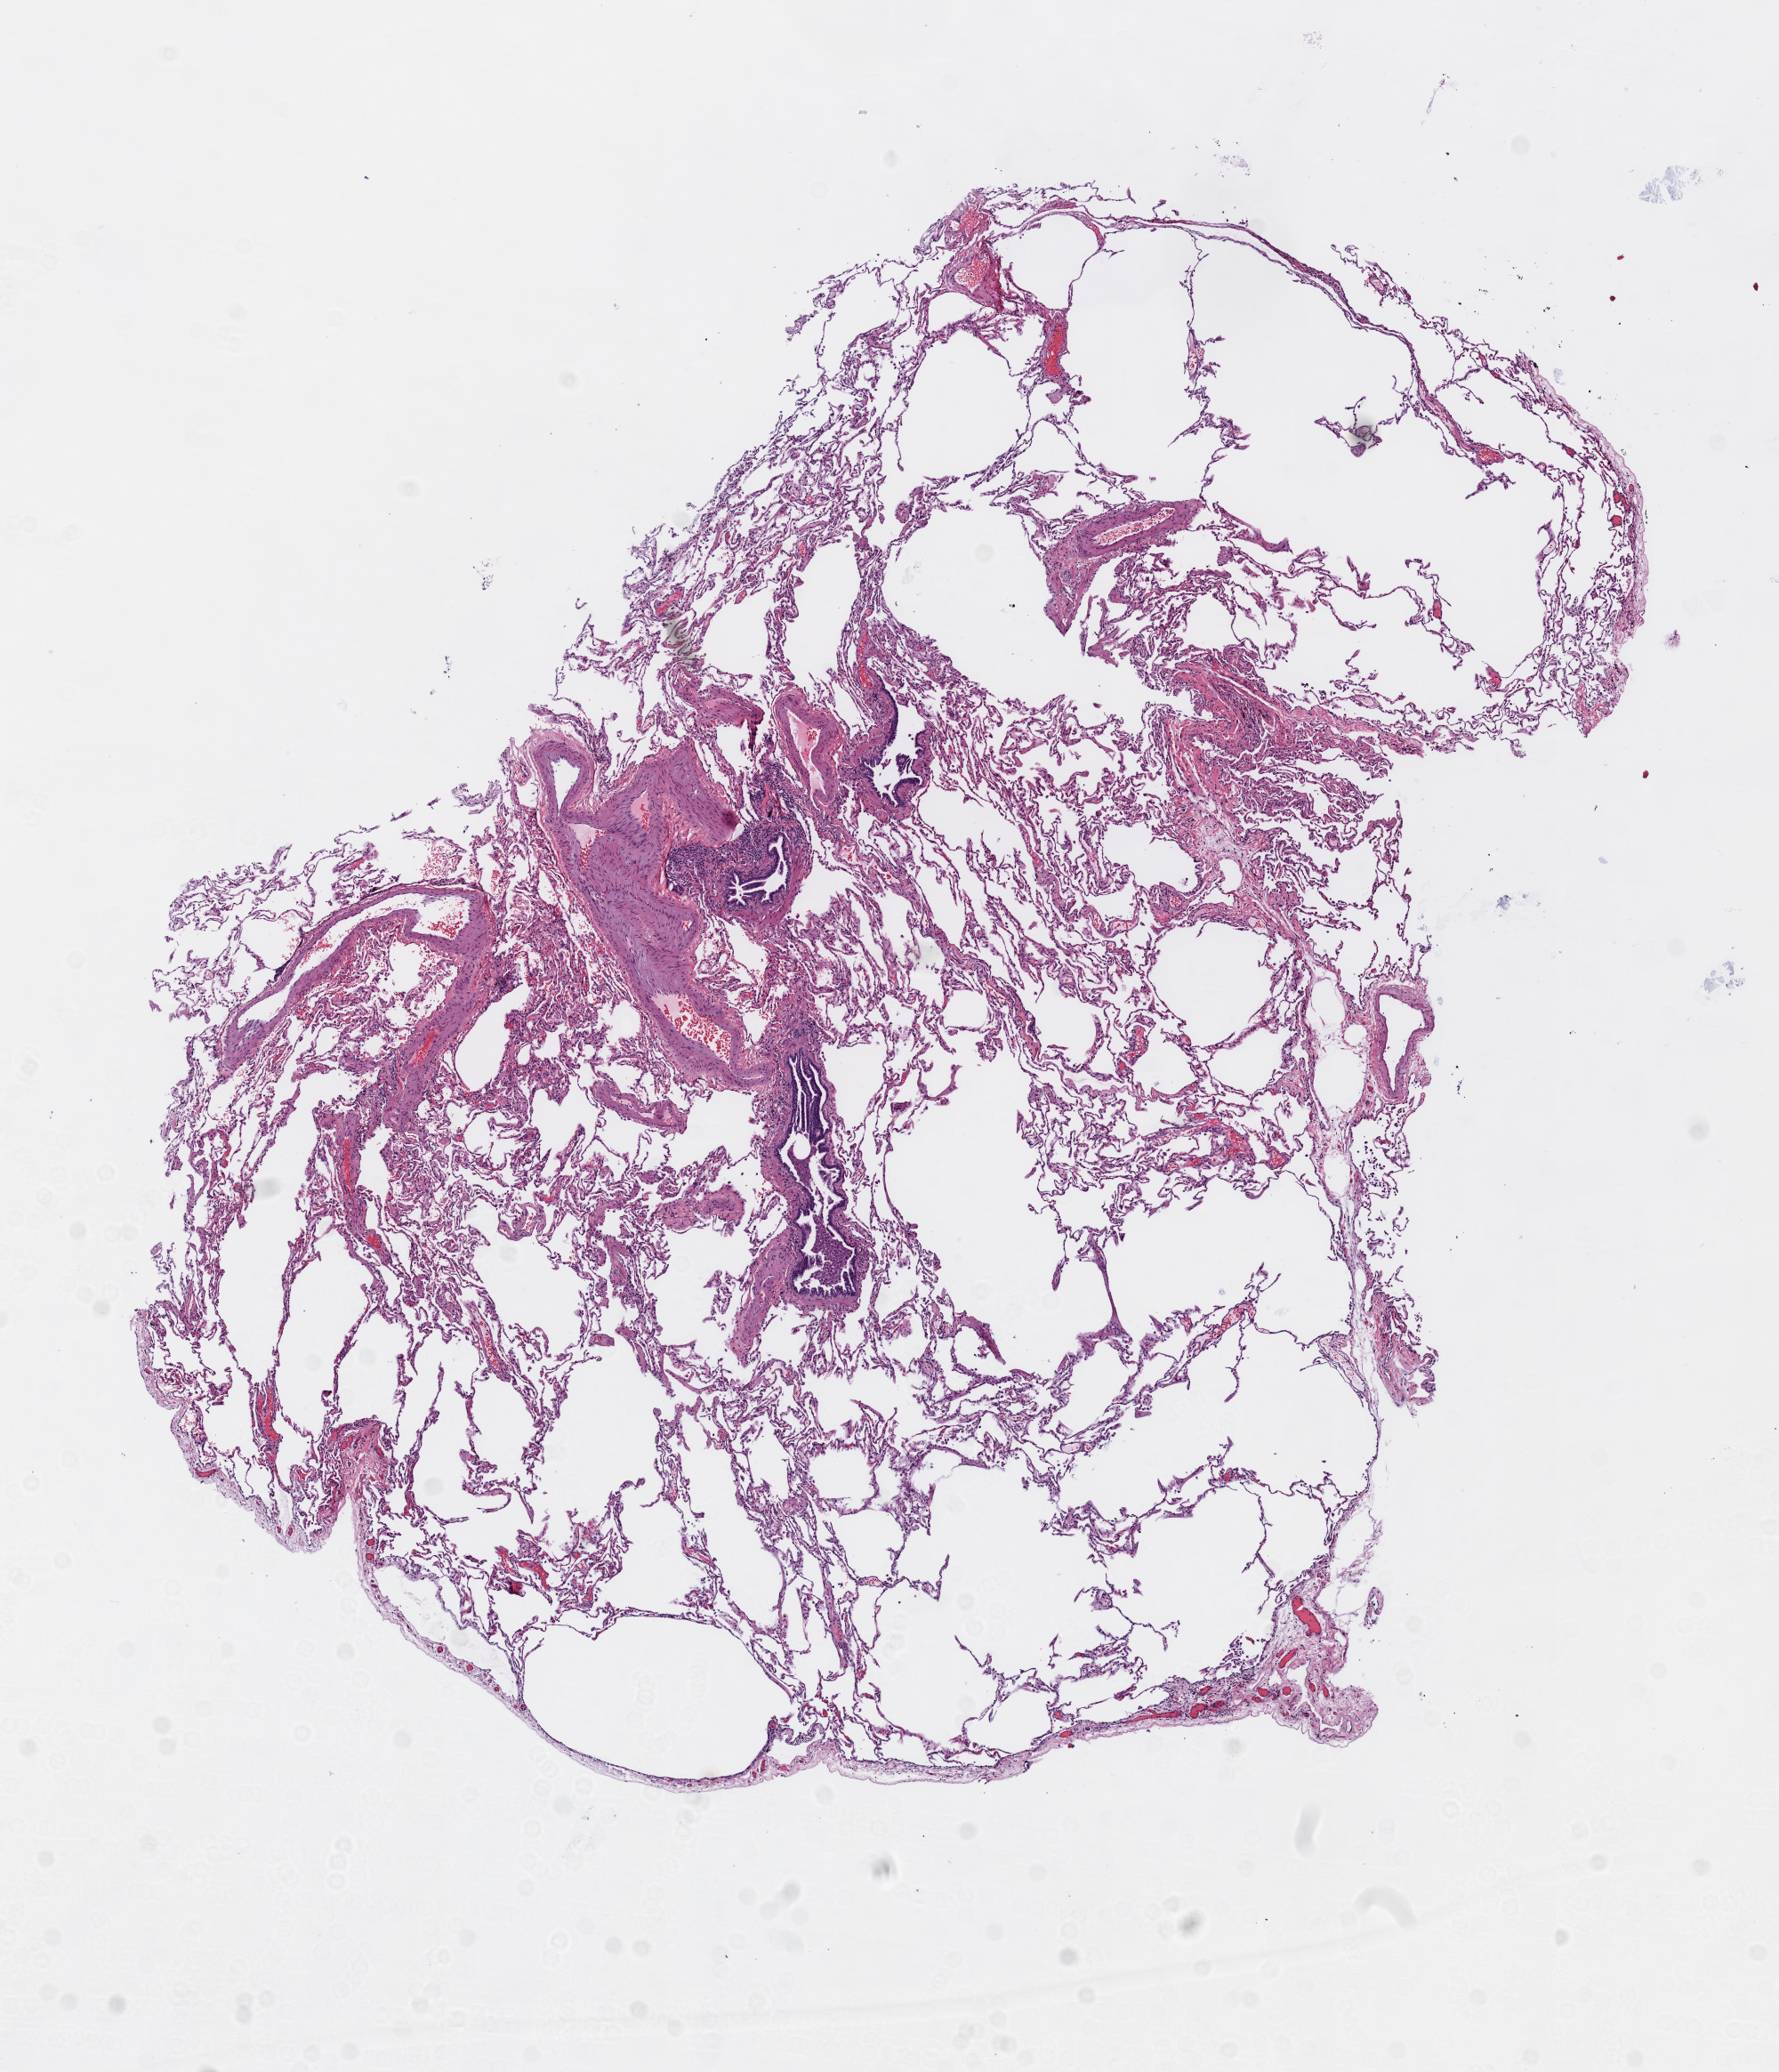
Hematoxylin and eosin (H&E) stained whole-slide image — a low-resolution overview of the entire scanned area, about 8.0 x 9.3 mm (slide scanned at 20x), frozen section from the top of the tissue portion, solid tissue normal (non-tumour tissue) sample from the lung. Female, age 62 years at initial diagnosis.
This section: solid tissue normal sample (biorepository sample class). Patient diagnosis: Squamous cell carcinoma, NOS (upper lobe, lung).